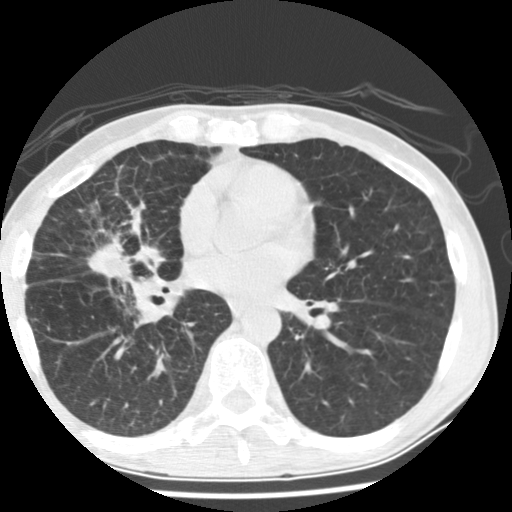
Low-dose screening chest CT, one axial slice. Position 77 of 162 along the scan axis. Reconstruction kernel STANDARD. Lung window (W 1500 / L -600 HU). 512 × 512 image matrix, field of view 310 × 310 mm.
Annotated regions visible in this slice (expert manual segmentation):
- lesion 1 (tumor, middle lobe of right lung): bounding box [x1, y1, x2, y2] px = [73, 235, 117, 282]